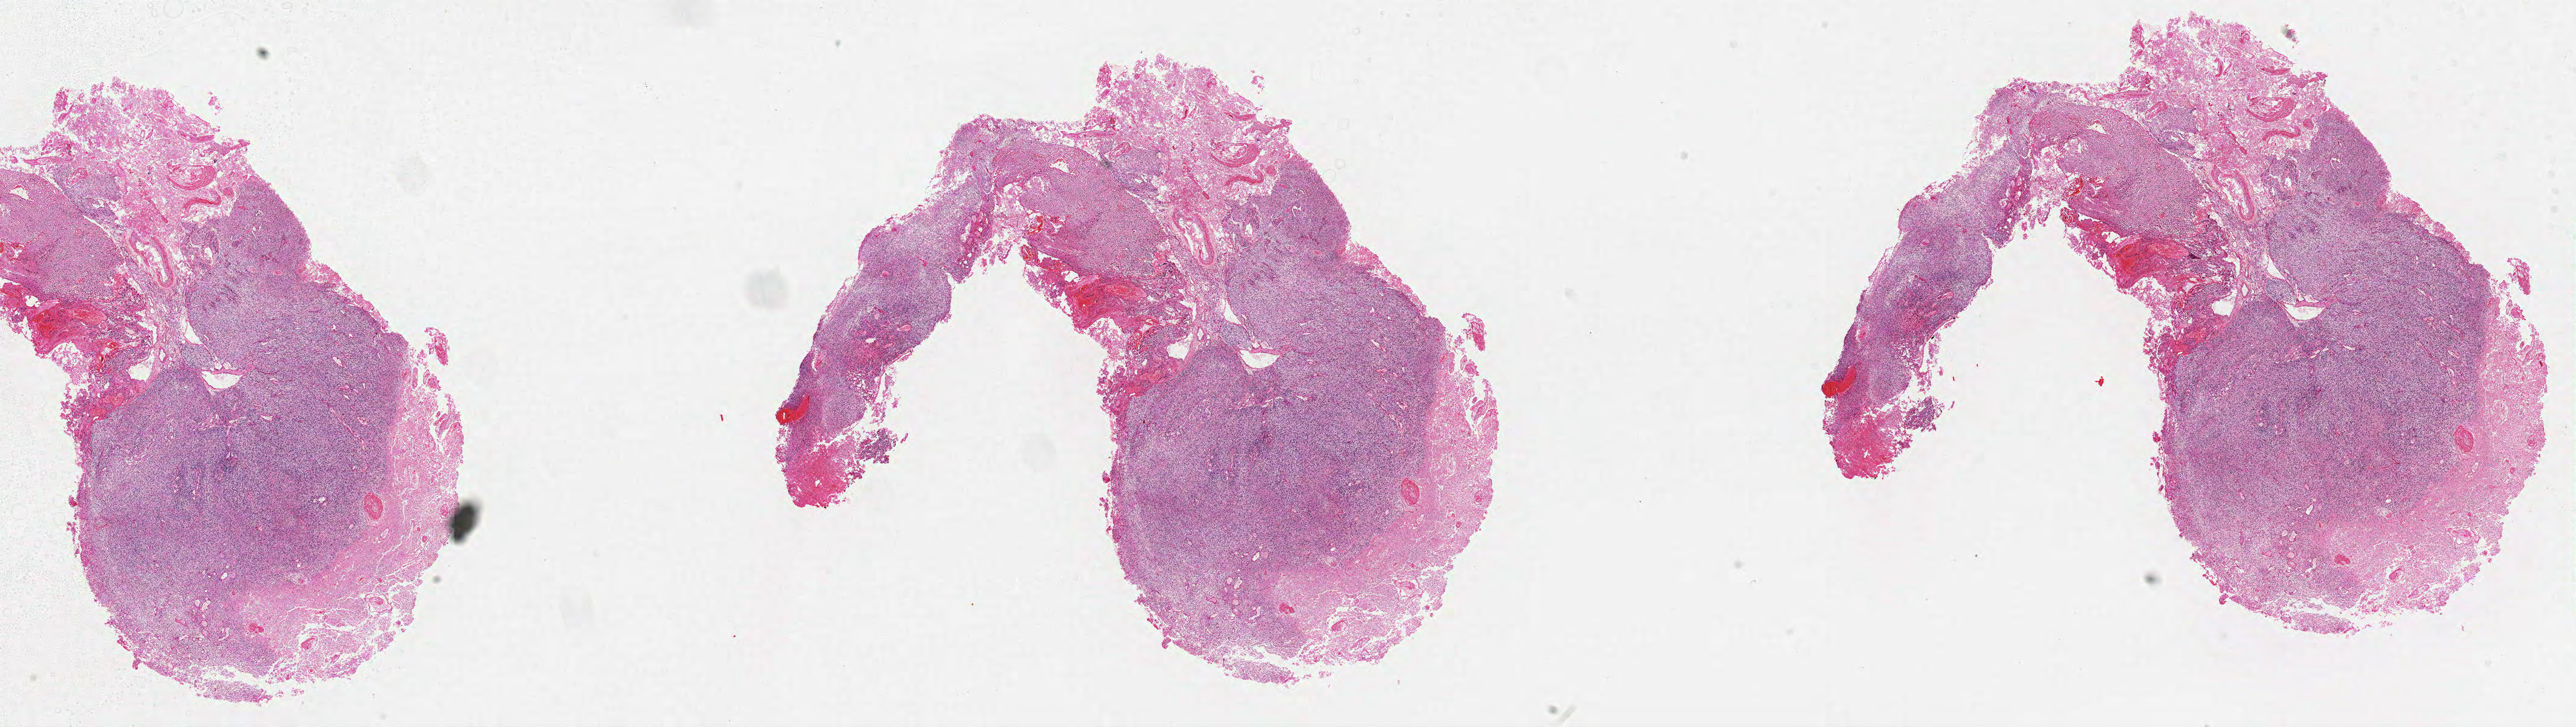
H&E-stained whole-slide image, whole scanned area (about 34.0 x 9.6 mm, slide scanned at 20x) shown as a low-resolution overview. Formalin-fixed paraffin-embedded (FFPE) diagnostic section. Brain, primary tumour sample. Patient: male, age at initial diagnosis 74 years.
* pathologic diagnosis: Glioblastoma